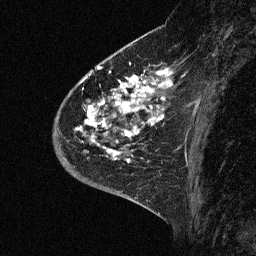
Breast MRI (dynamic contrast-enhanced), one sagittal slice; slice 20 of 64 in the series (ordered by position); dynamic contrast-enhanced study with each time point stored as its own series, time point 2 of 3 at this slice position (early post-contrast, ordered by acquisition time); 1.5 T; TE 4.5 ms, TR 11 ms; 2.06 mm slice thickness; 256 × 256 image matrix, field of view 200 × 200 mm. Patient: female, 46 years. From the clinical record (not read from this slice): setting: breast cancer imaged before/during neoadjuvant chemotherapy; receptor status: HER2-positive.
Annotated regions visible in this slice (semi-automatically segmented with operator editing):
- analysis volume of interest (the breast-tissue region the enhancement analysis was run in; not a lesion): bounding box <43,72,176,177> (left, top, right, bottom; pixels)
- tumour enhancement mask (voxels above the 90 % enhancement threshold inside the analysis volume of interest): <75,72,172,164>